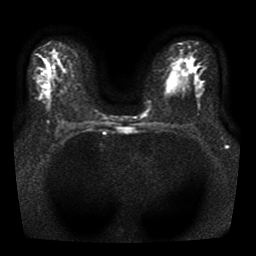
Breast MRI, one axial slice. Slice 26 of 41 in the series (ordered by position). Diffusion-weighted series; image 2 of 4 stored at this slice position (different b-values; order by instance number). 1.5 T. 5 mm slice thickness. 256 × 256 image matrix, field of view 330 × 330 mm. Female patient.
Outlined on this slice (expert manual segmentation):
- tumour on diffusion-weighted imaging: box from (x=44, y=94) to (x=49, y=98) px